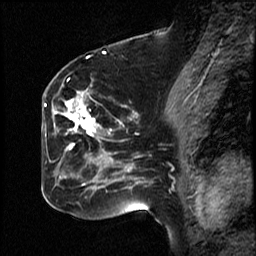
Breast MRI (dynamic contrast-enhanced), one sagittal slice; dynamic contrast-enhanced study with each time point stored as its own series, time point 2 of 4 at this slice position (early post-contrast, ordered by acquisition time); 1.5 T; TE 4.2 ms, TR 18.5 ms; 3 mm slice thickness; 256 × 256 image matrix, field of view 200 × 200 mm. Patient: female, 44 years. Case-level facts recorded for this patient, not image findings: setting: breast cancer imaged before/during neoadjuvant chemotherapy; receptor status: HR-positive, HER2-negative.
Structures marked on this image (semi-automatically segmented with operator editing):
- analysis volume of interest (the breast-tissue region the enhancement analysis was run in; not a lesion): box from (x=59, y=80) to (x=114, y=206) px
- tumour enhancement mask (voxels above the 100 % enhancement threshold inside the analysis volume of interest): (x=64, y=92)–(x=99, y=151)